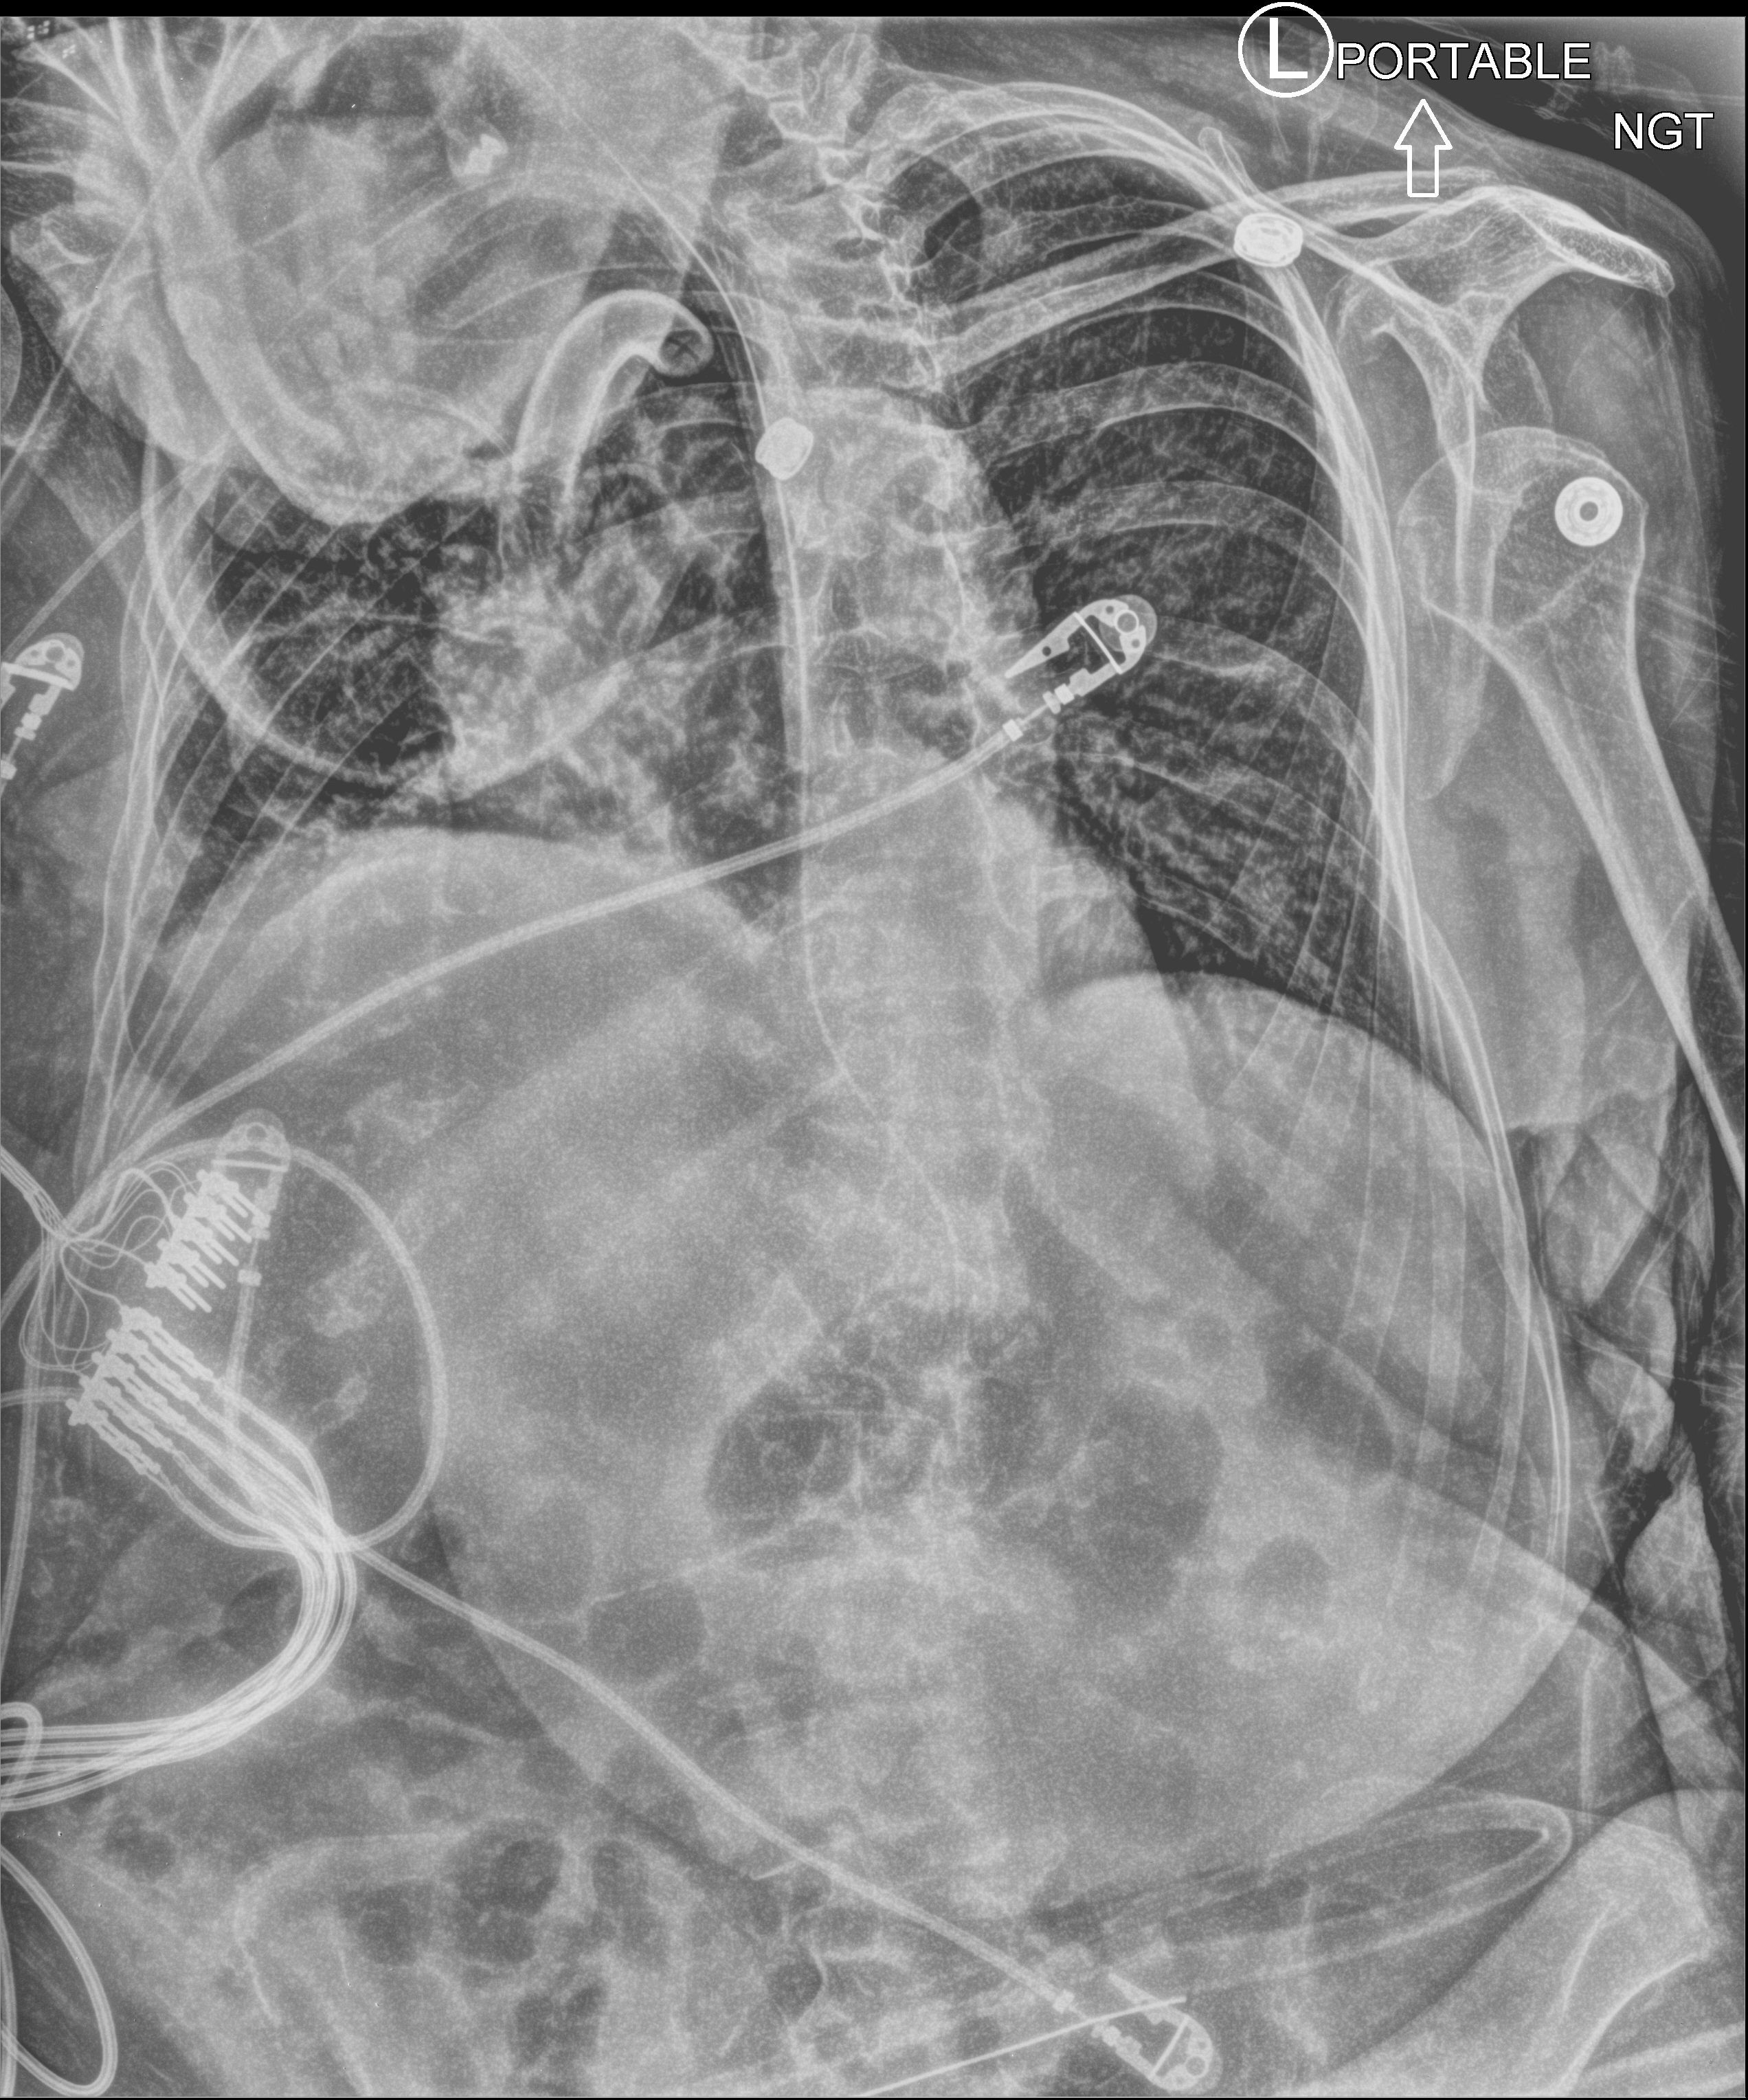
Abdomen X-ray (portable); anteroposterior (AP) projection. Female patient hospitalised with COVID-19, age 75–90 years.
Admission-level facts for this patient (not findings on this image; timing relative to this image not recorded): smoking status (admission record): former.